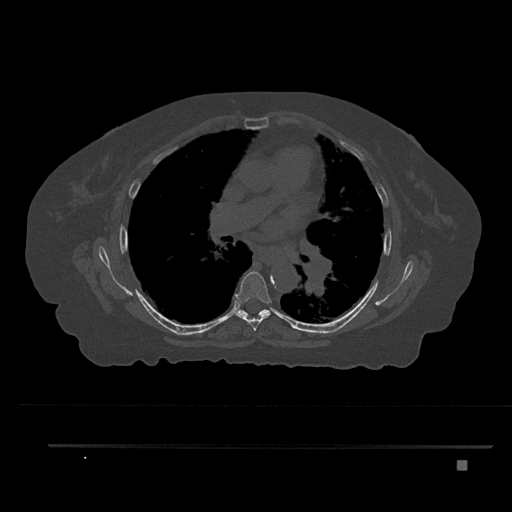
CT including the spine, one axial slice. Position 516 of 797 along the scan axis. 120 kVp. Bone window (W 1800 / L 400 HU). 512 × 512 image matrix. Patient: female, 76 years. Case-level facts recorded for this patient, not image findings: primary cancer: lung; vertebrae with lytic lesions (as recorded): T11, L3.
Annotated regions visible in this slice (semi-automatic segmentation, software-assisted and operator-edited):
- T6 vertebra: bounding box (x1, y1, x2, y2) in pixels: (235, 271, 271, 331)
- T7 vertebra: (238, 309, 269, 317)